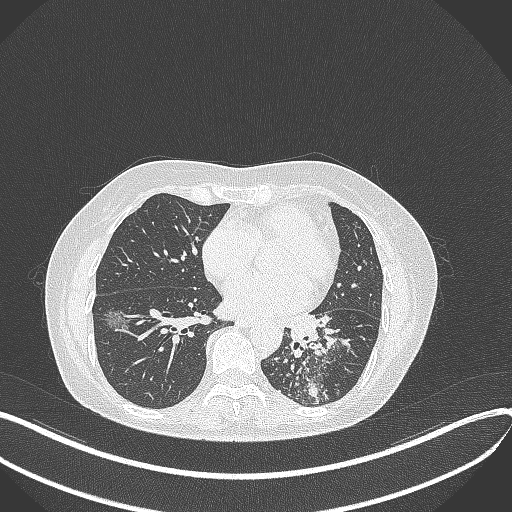
Chest CT, one axial slice. Slice 169 of 429 in the series (ordered by position). Reconstruction kernel B70f. Lung window (W 1500 / L -600 HU). 512 × 512 image matrix, field of view 400 × 400 mm. Female patient, age 63 years. Case-level facts recorded for this patient, not image findings: clinical TNM (as recorded): T1b N0 M0.
Outlined on this slice (bounding box drawn by a radiologist):
- lung tumour (recorded histology: adenocarcinoma): bounding box (x1, y1, x2, y2) in pixels: (277, 307, 344, 361)